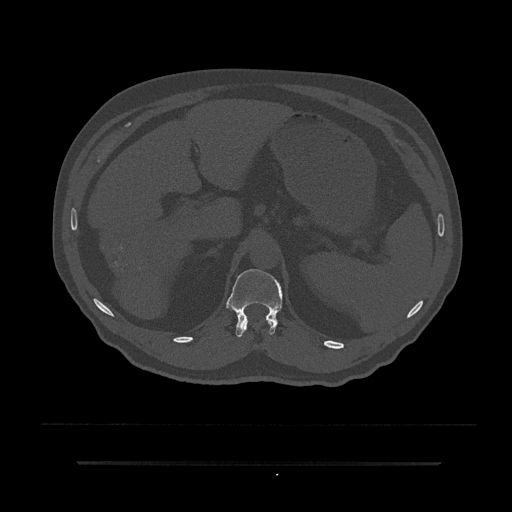
CT including the spine, one axial slice. Position 229 of 797 along the scan axis. Reconstruction kernel Br40s/3. 120 kVp. Bone window (W 1800 / L 400 HU). 0.5 mm slice thickness. 512 × 512 image matrix. Patient: male, 59 years. From the clinical record (not read from this slice): primary cancer: bile ducts; vertebrae with lytic lesions (as recorded): T10.
Annotated regions visible in this slice (semi-automatic segmentation, software-assisted and operator-edited):
- T11 vertebra: bounding box [x1, y1, x2, y2] px = [244, 321, 274, 329]
- T12 vertebra: [226, 269, 283, 337]